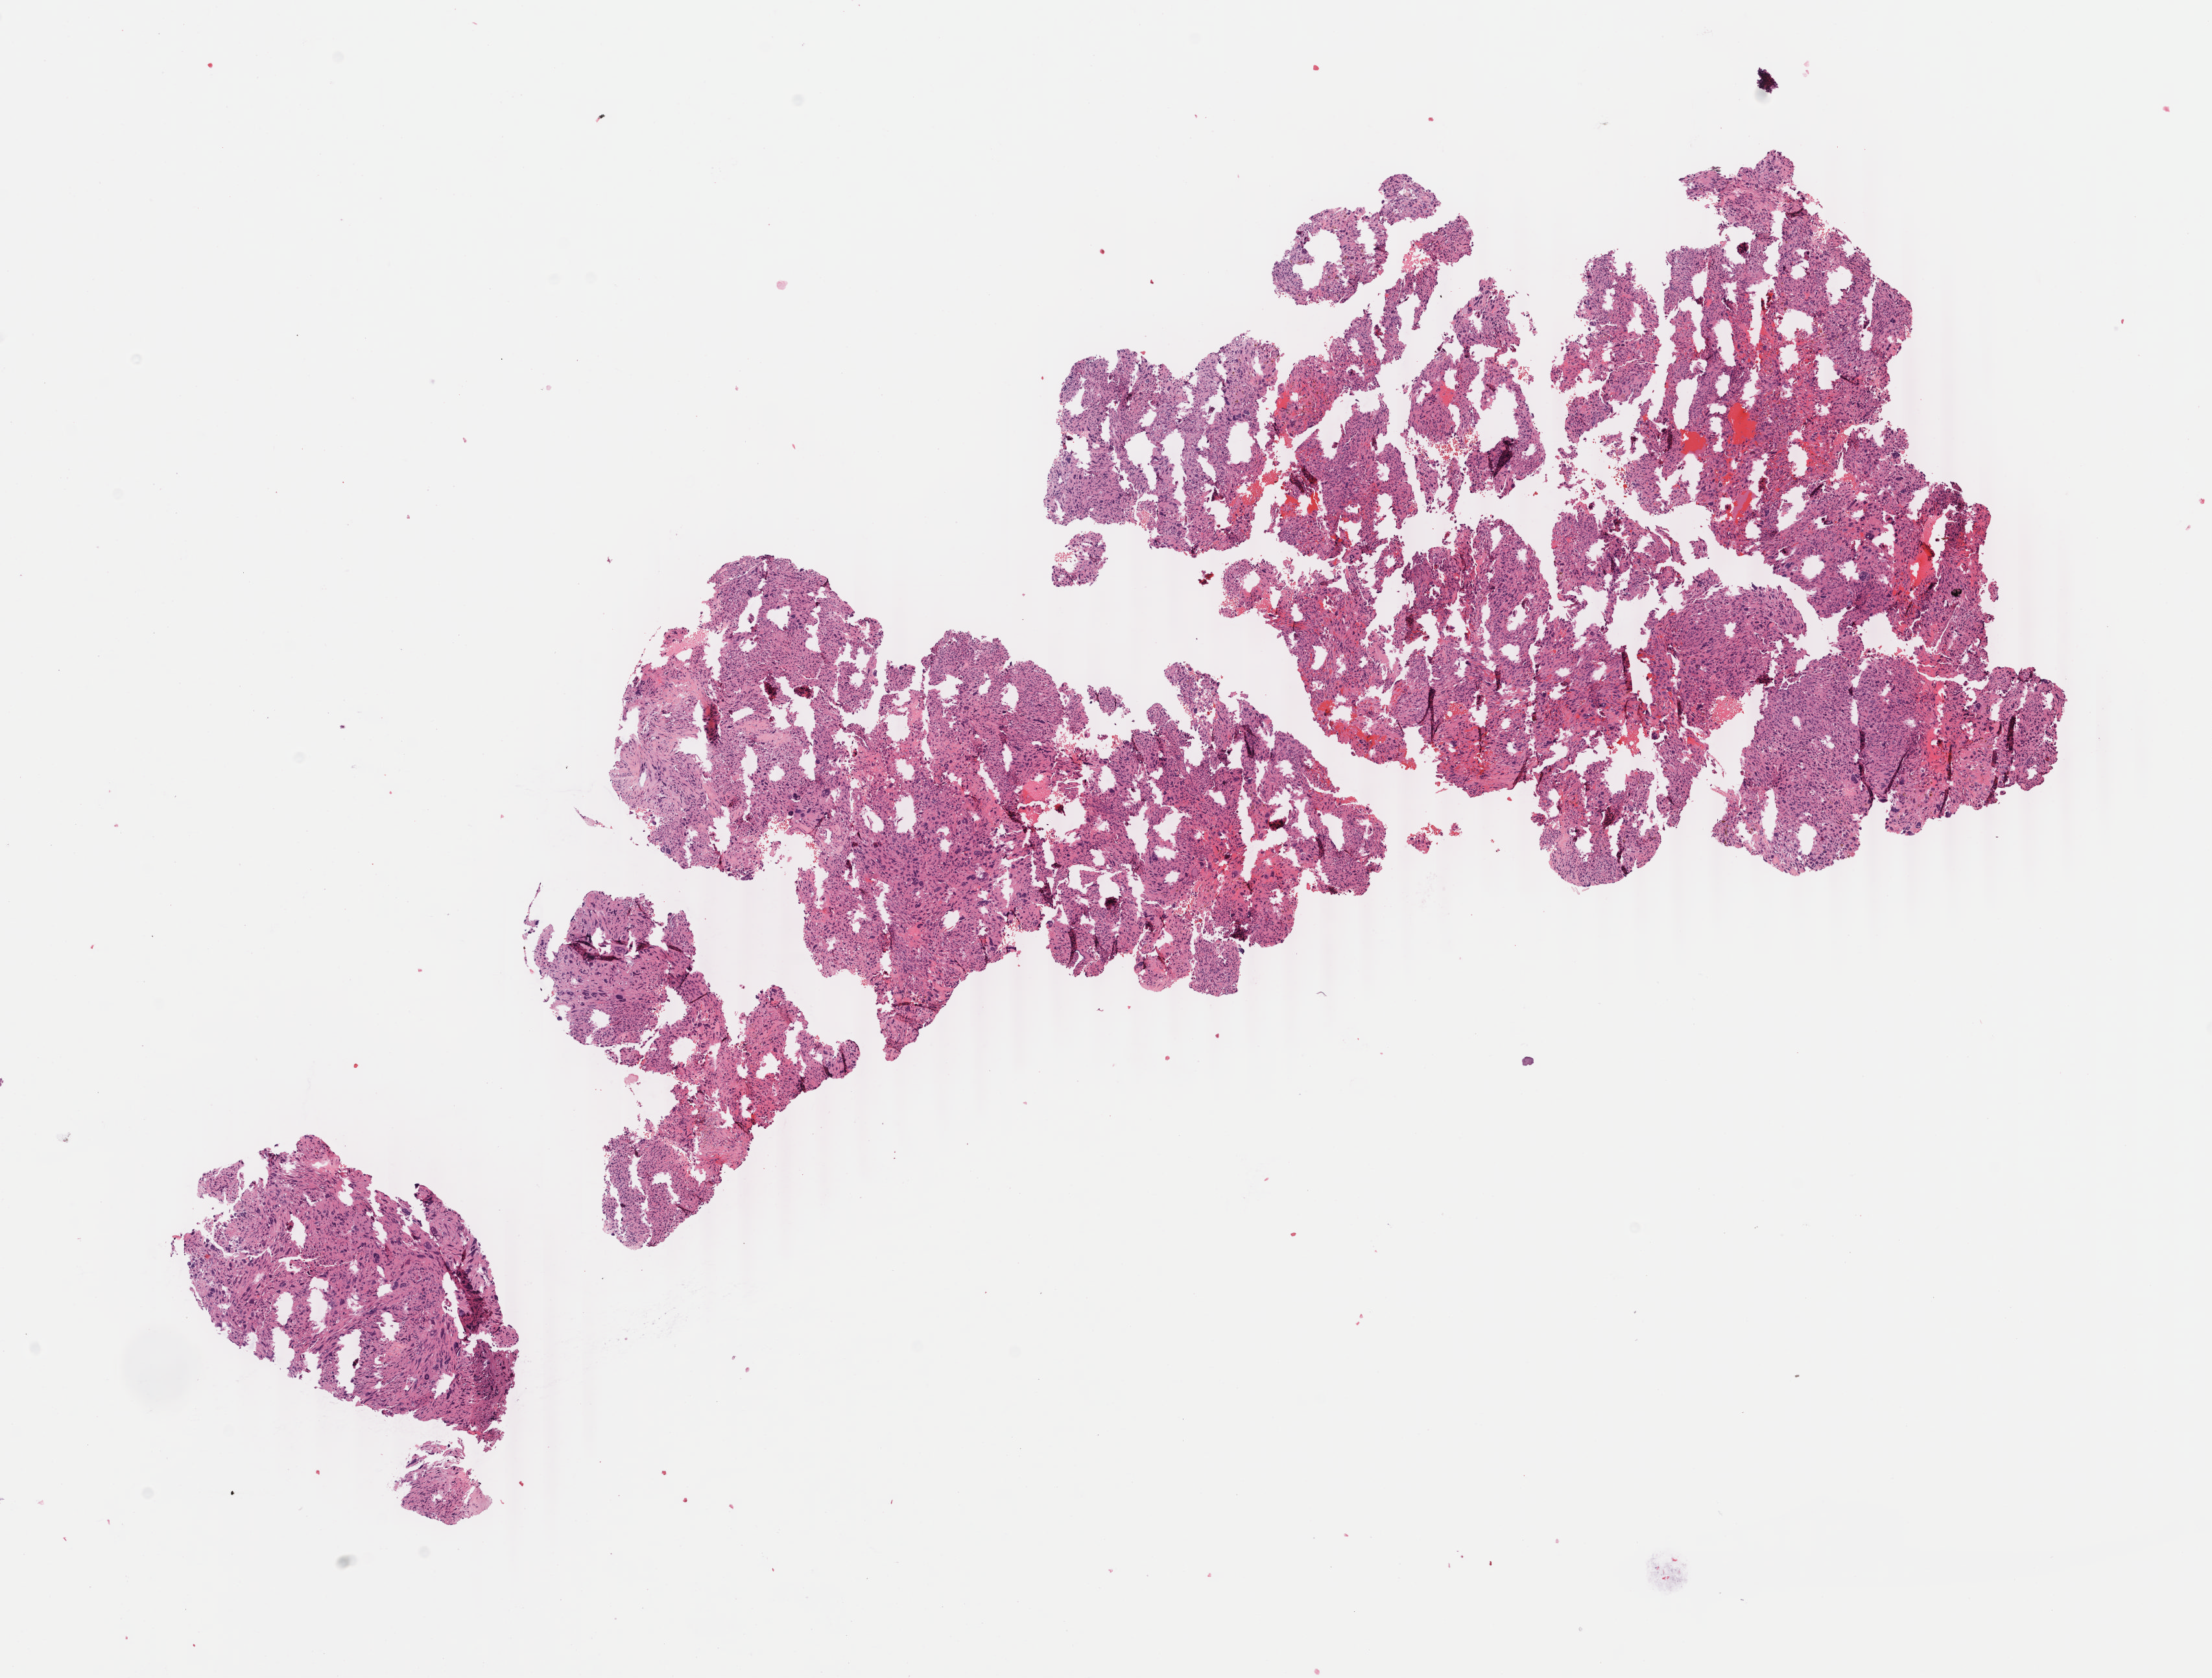
Digitized Hematoxylin and eosin (H&E) stained tissue section (whole slide), low-resolution overview of the scanned area, about 13.6 x 10.3 mm (slide scanned at 40x). FFPE section. Primary tumour sample from the connective, subcutaneous and other soft tissues. Female, age 67 years at initial diagnosis.
Pathologic diagnosis: Leiomyosarcoma, NOS (connective, subcutaneous and other soft tissues of lower limb and hip).